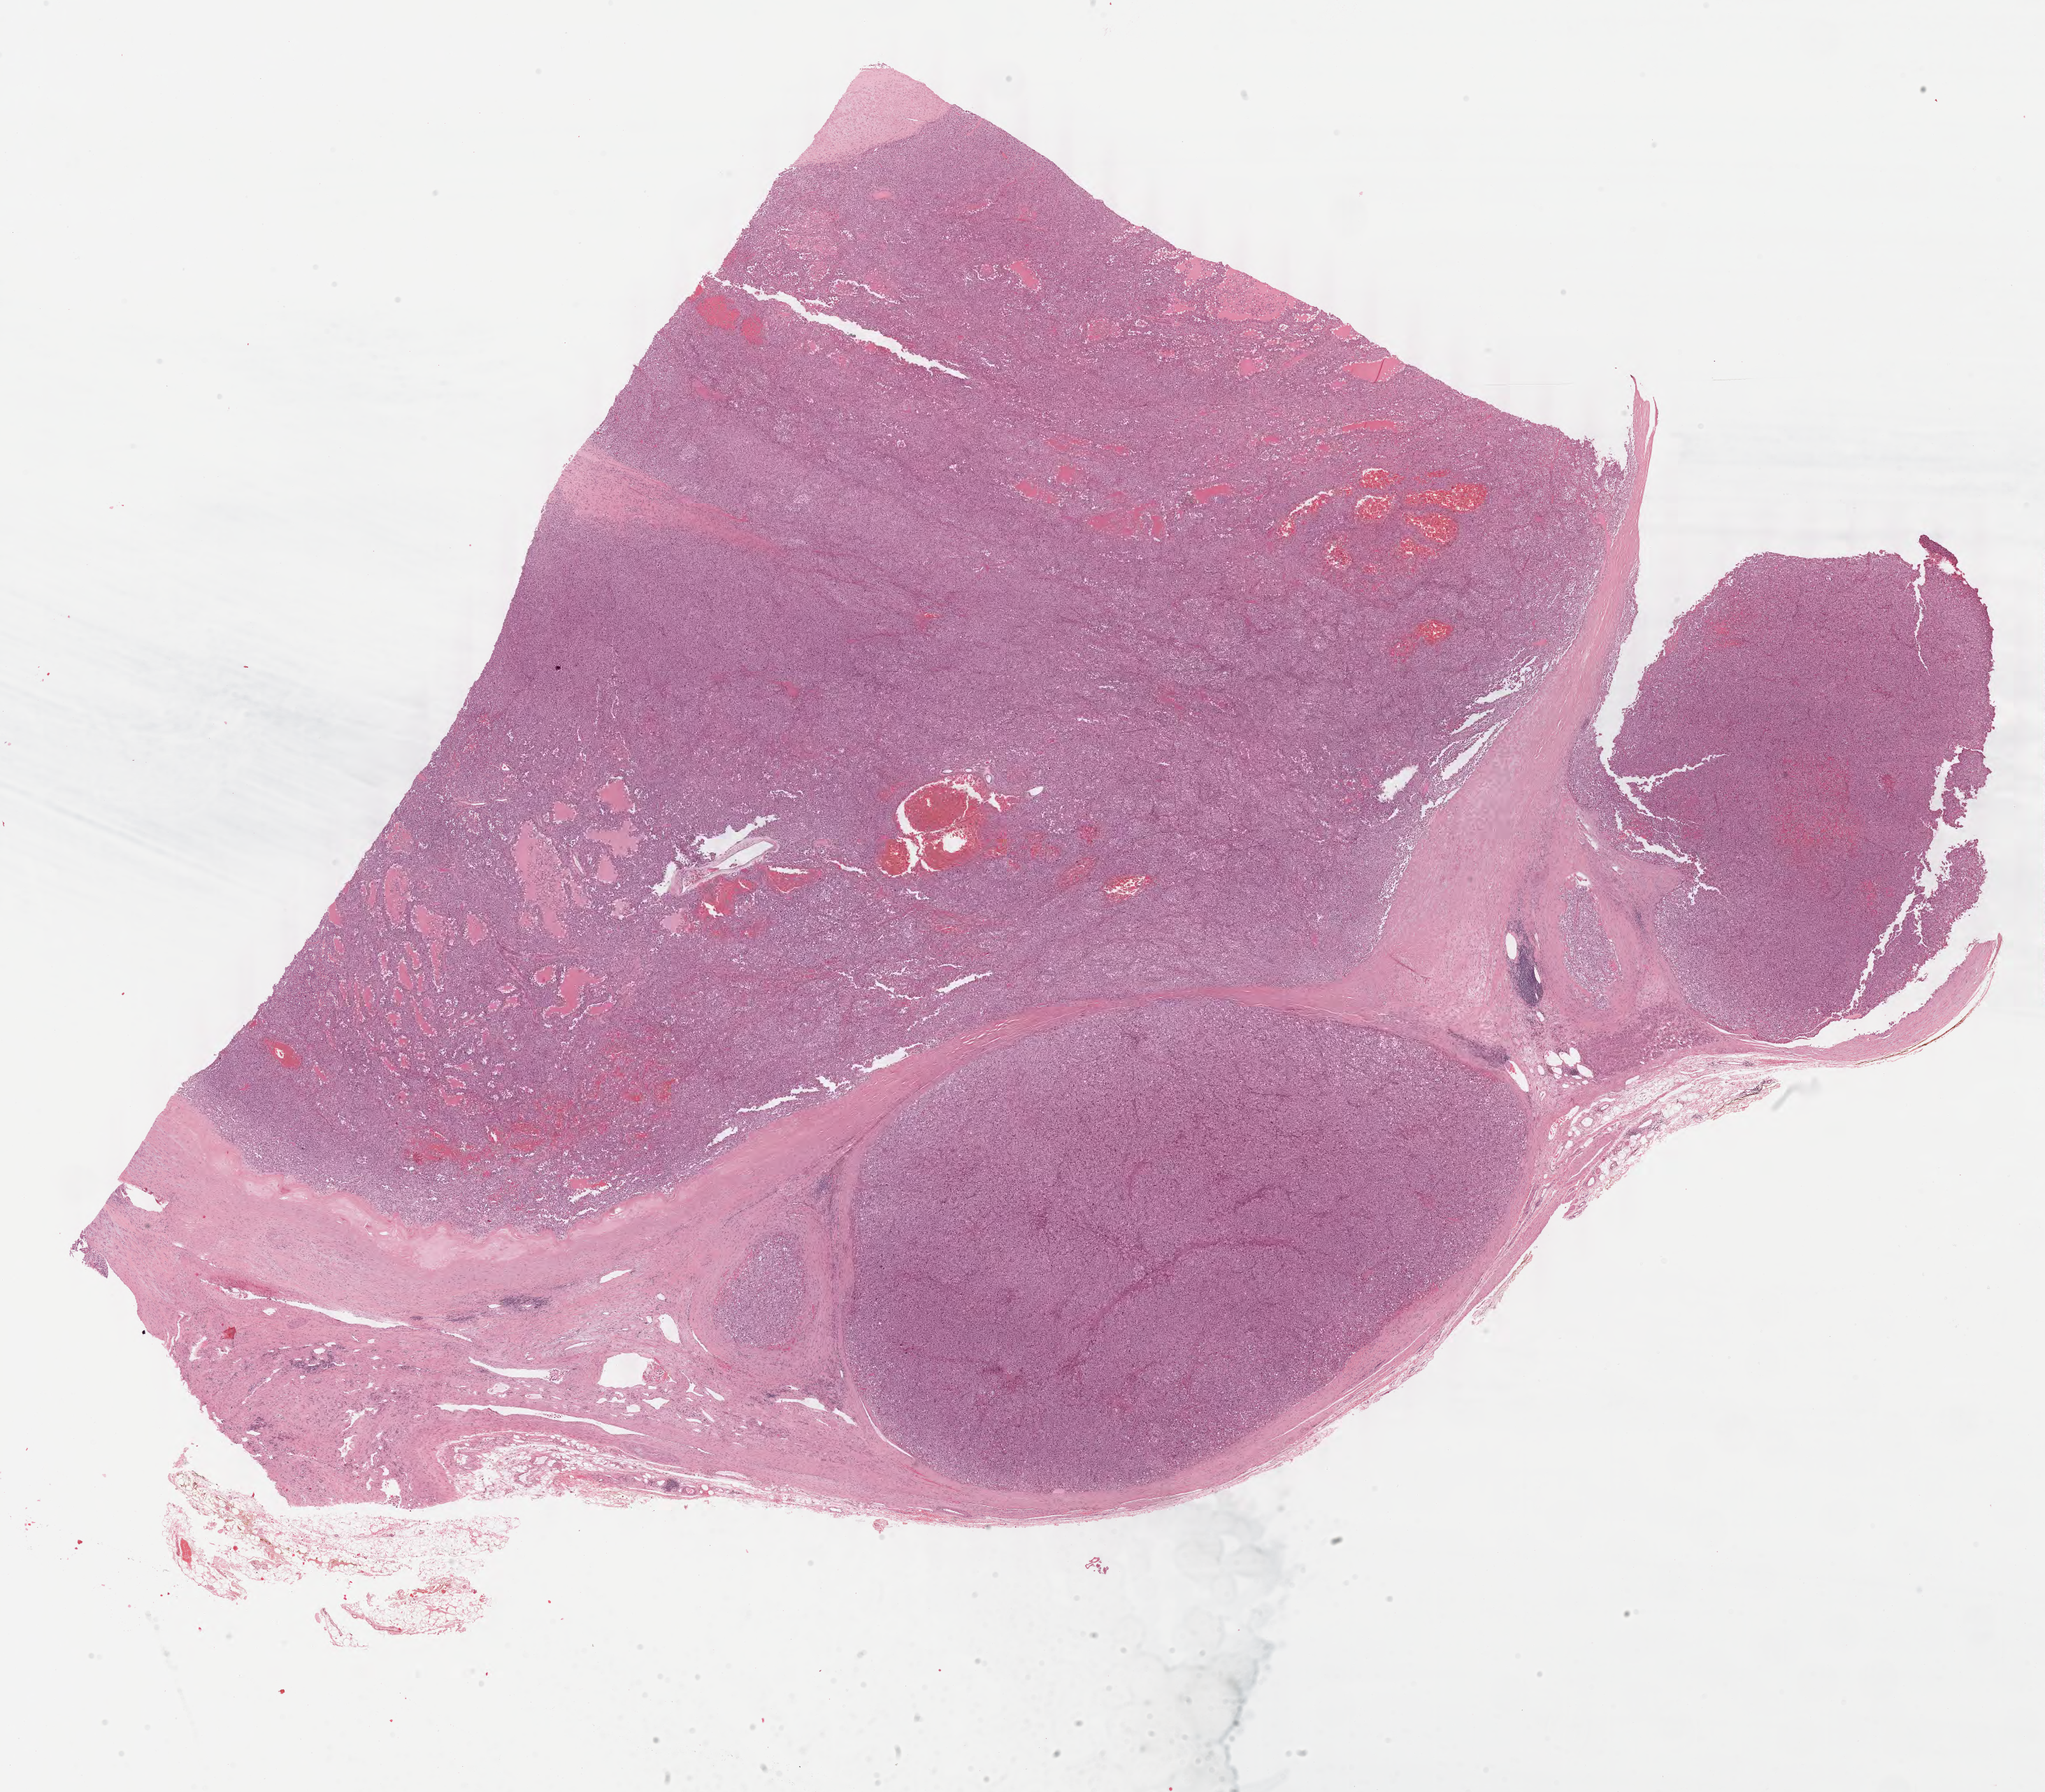
Digitized Hematoxylin and eosin (H&E) stained tissue section (whole slide), low-resolution overview of the scanned area, about 23.1 x 20.2 mm (from a 40x scan). Formalin-fixed paraffin-embedded (FFPE) diagnostic section. Adrenal cortex, primary tumour sample. Patient: male, age at initial diagnosis 63 years.
Pathologic diagnosis: Adrenal cortical carcinoma.